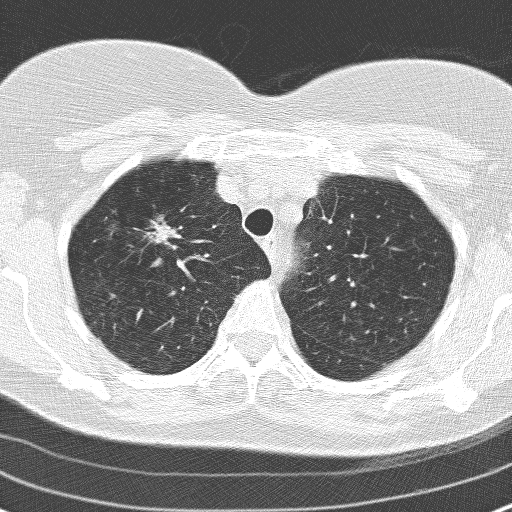
Low-dose screening chest CT, one axial slice. Position 126 of 160 along the scan axis. 120 kVp. Lung window (W 1500 / L -600 HU). 3.2 mm slice thickness. 512 × 512 image matrix, field of view 313 × 313 mm.
Annotated regions visible in this slice (outlined manually by an expert reader):
- lesion 1 (tumor, upper lobe of right lung): bounding box [x1, y1, x2, y2] px = [151, 222, 172, 243]